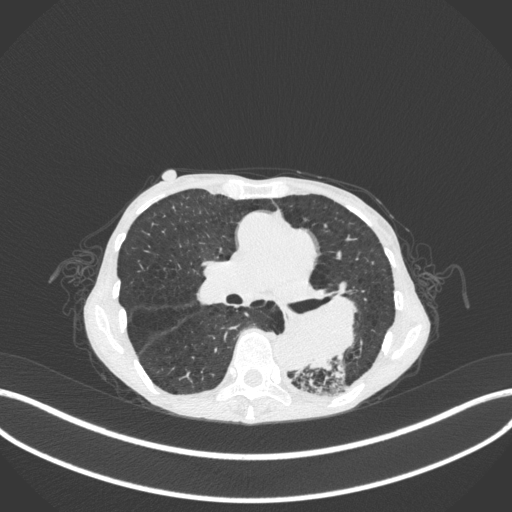
Chest CT, one axial slice; reconstruction kernel B31f; lung window (W 1500 / L -600 HU); 1 mm slice thickness; 512 × 512 image matrix, field of view 400 × 400 mm. Female patient, age 70 years. Case-level facts recorded for this patient, not image findings: clinical TNM (as recorded): T3 N0 M0.
Structures marked on this image (rectangle marked by the reading radiologist):
- lung tumour (recorded histology: small cell carcinoma): bounding box (x1, y1, x2, y2) in pixels: (276, 287, 362, 372)